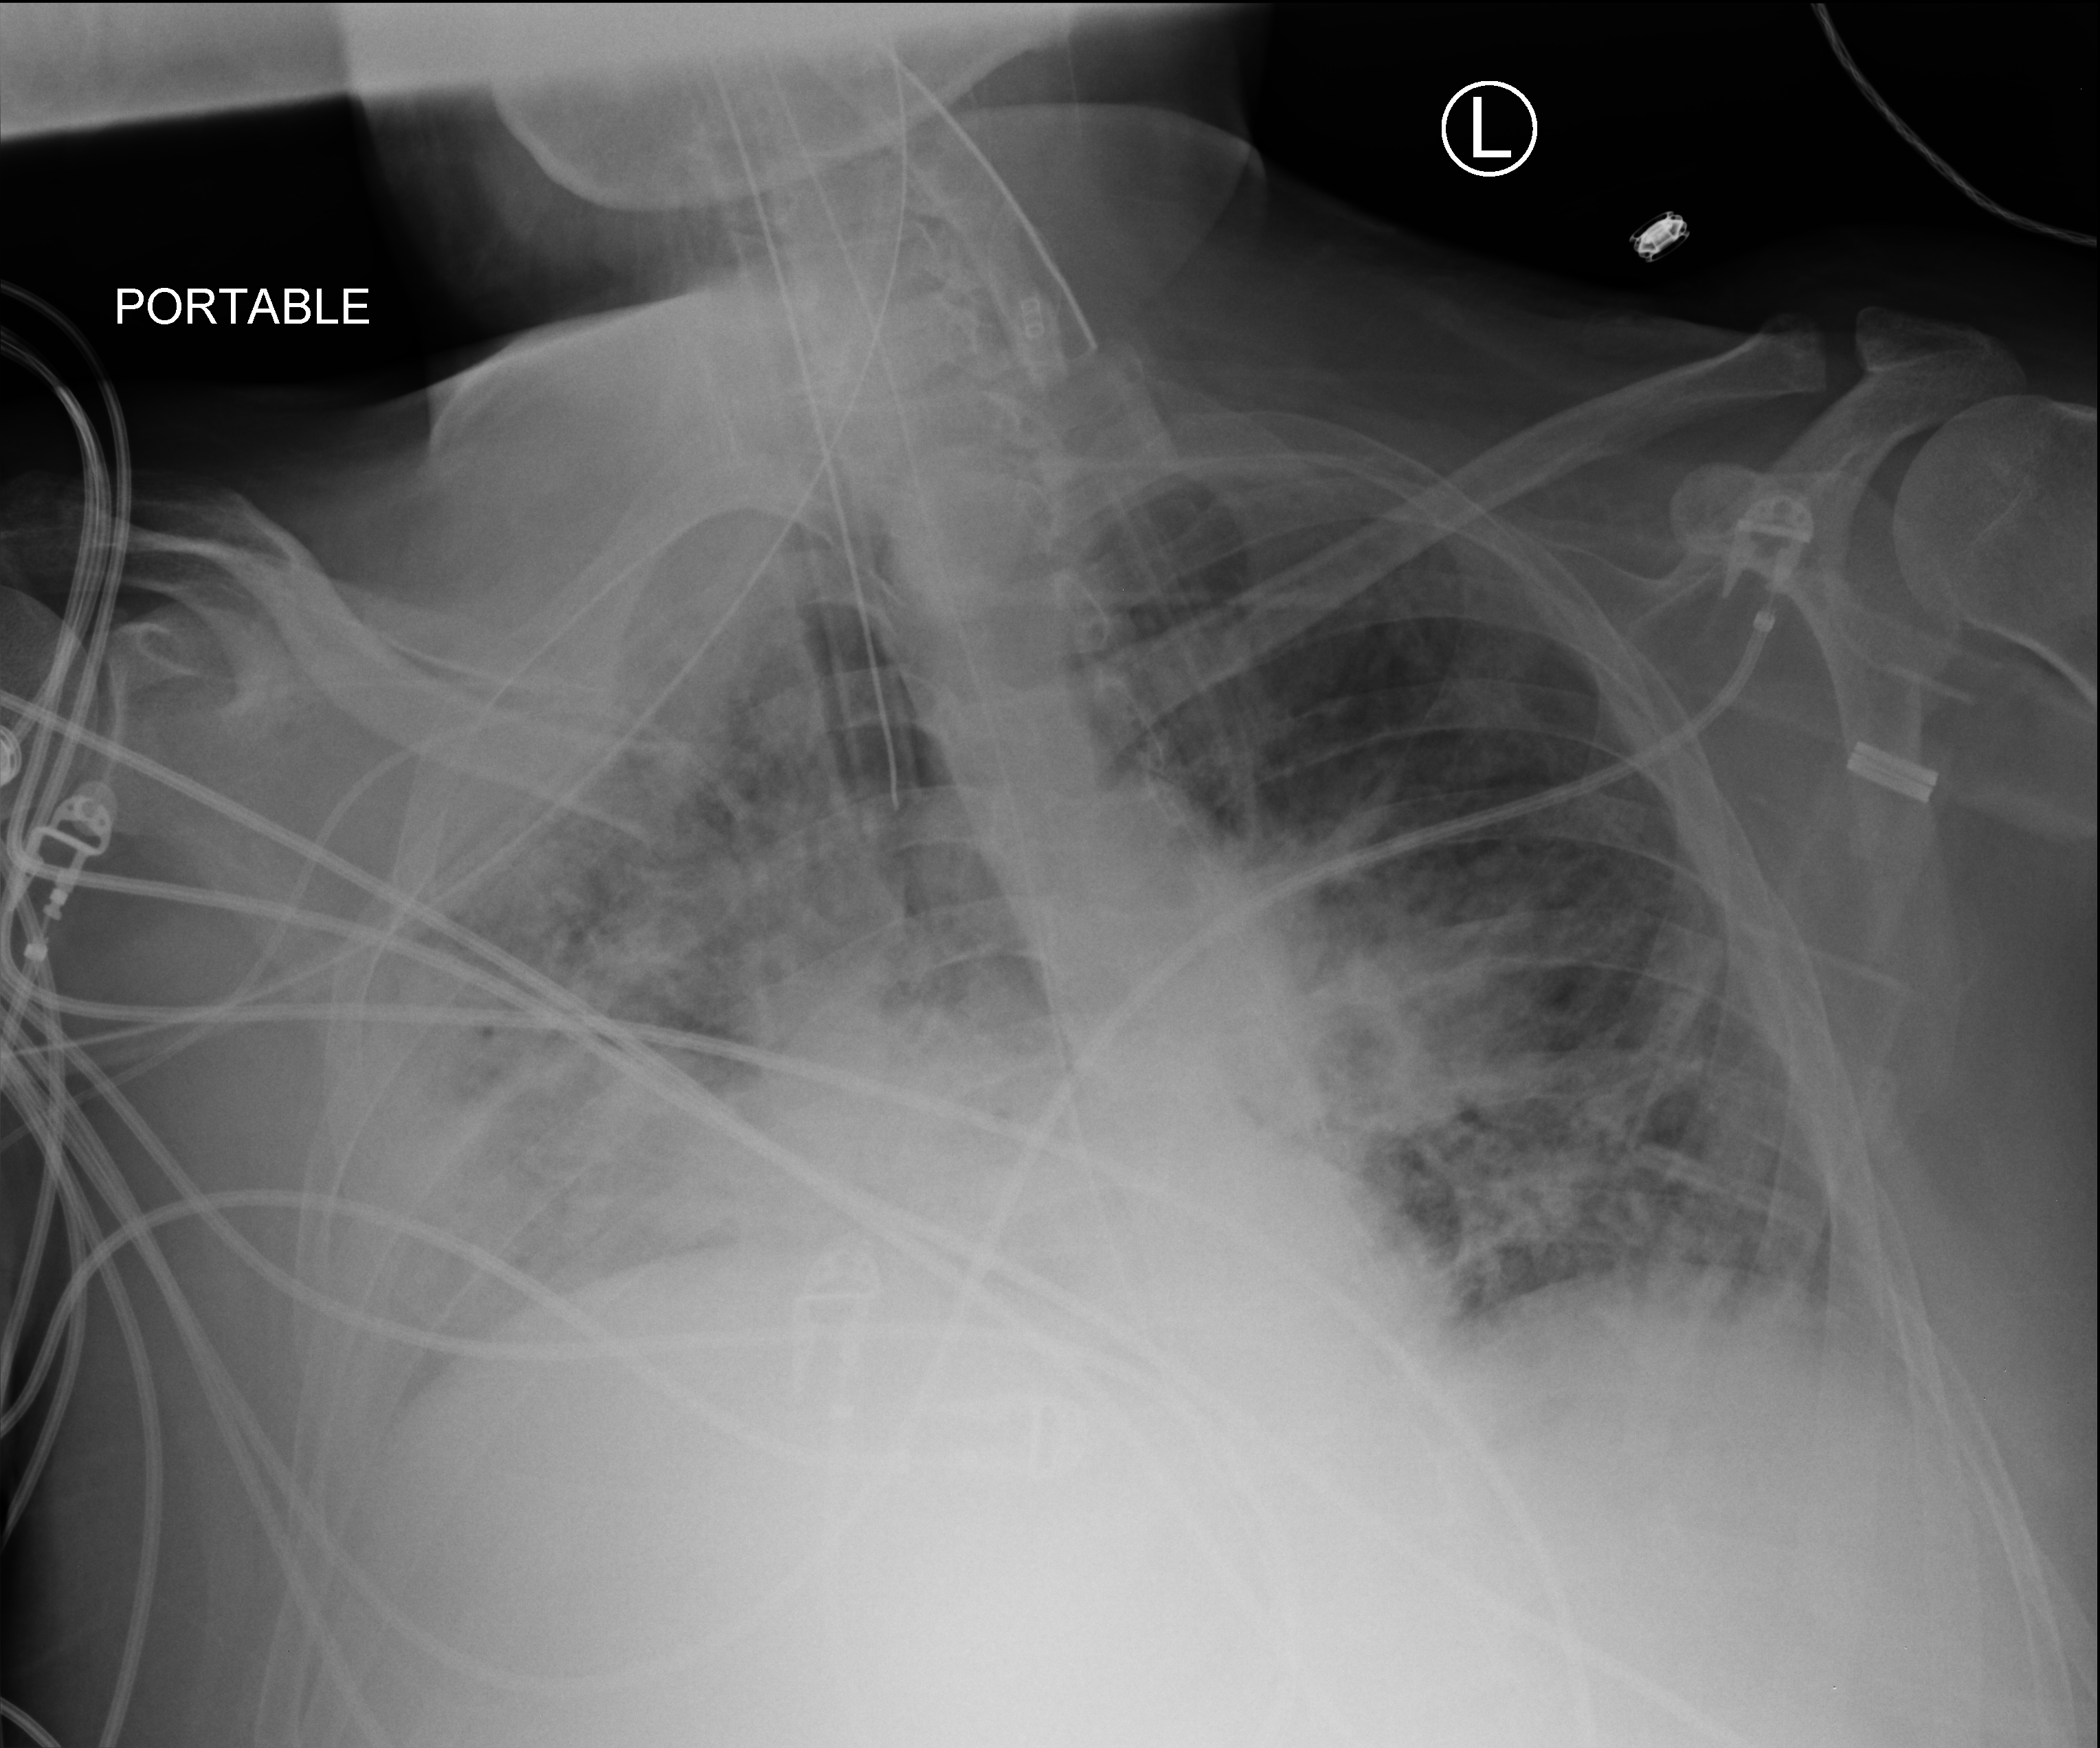
Chest X-ray (portable), anteroposterior (AP) projection. Adult patient hospitalised with COVID-19, age 18–59 years.
Admission-level facts for this patient (not findings on this image; timing relative to this image not recorded):
- smoking status (admission record): never
- hypertension (admission record): yes